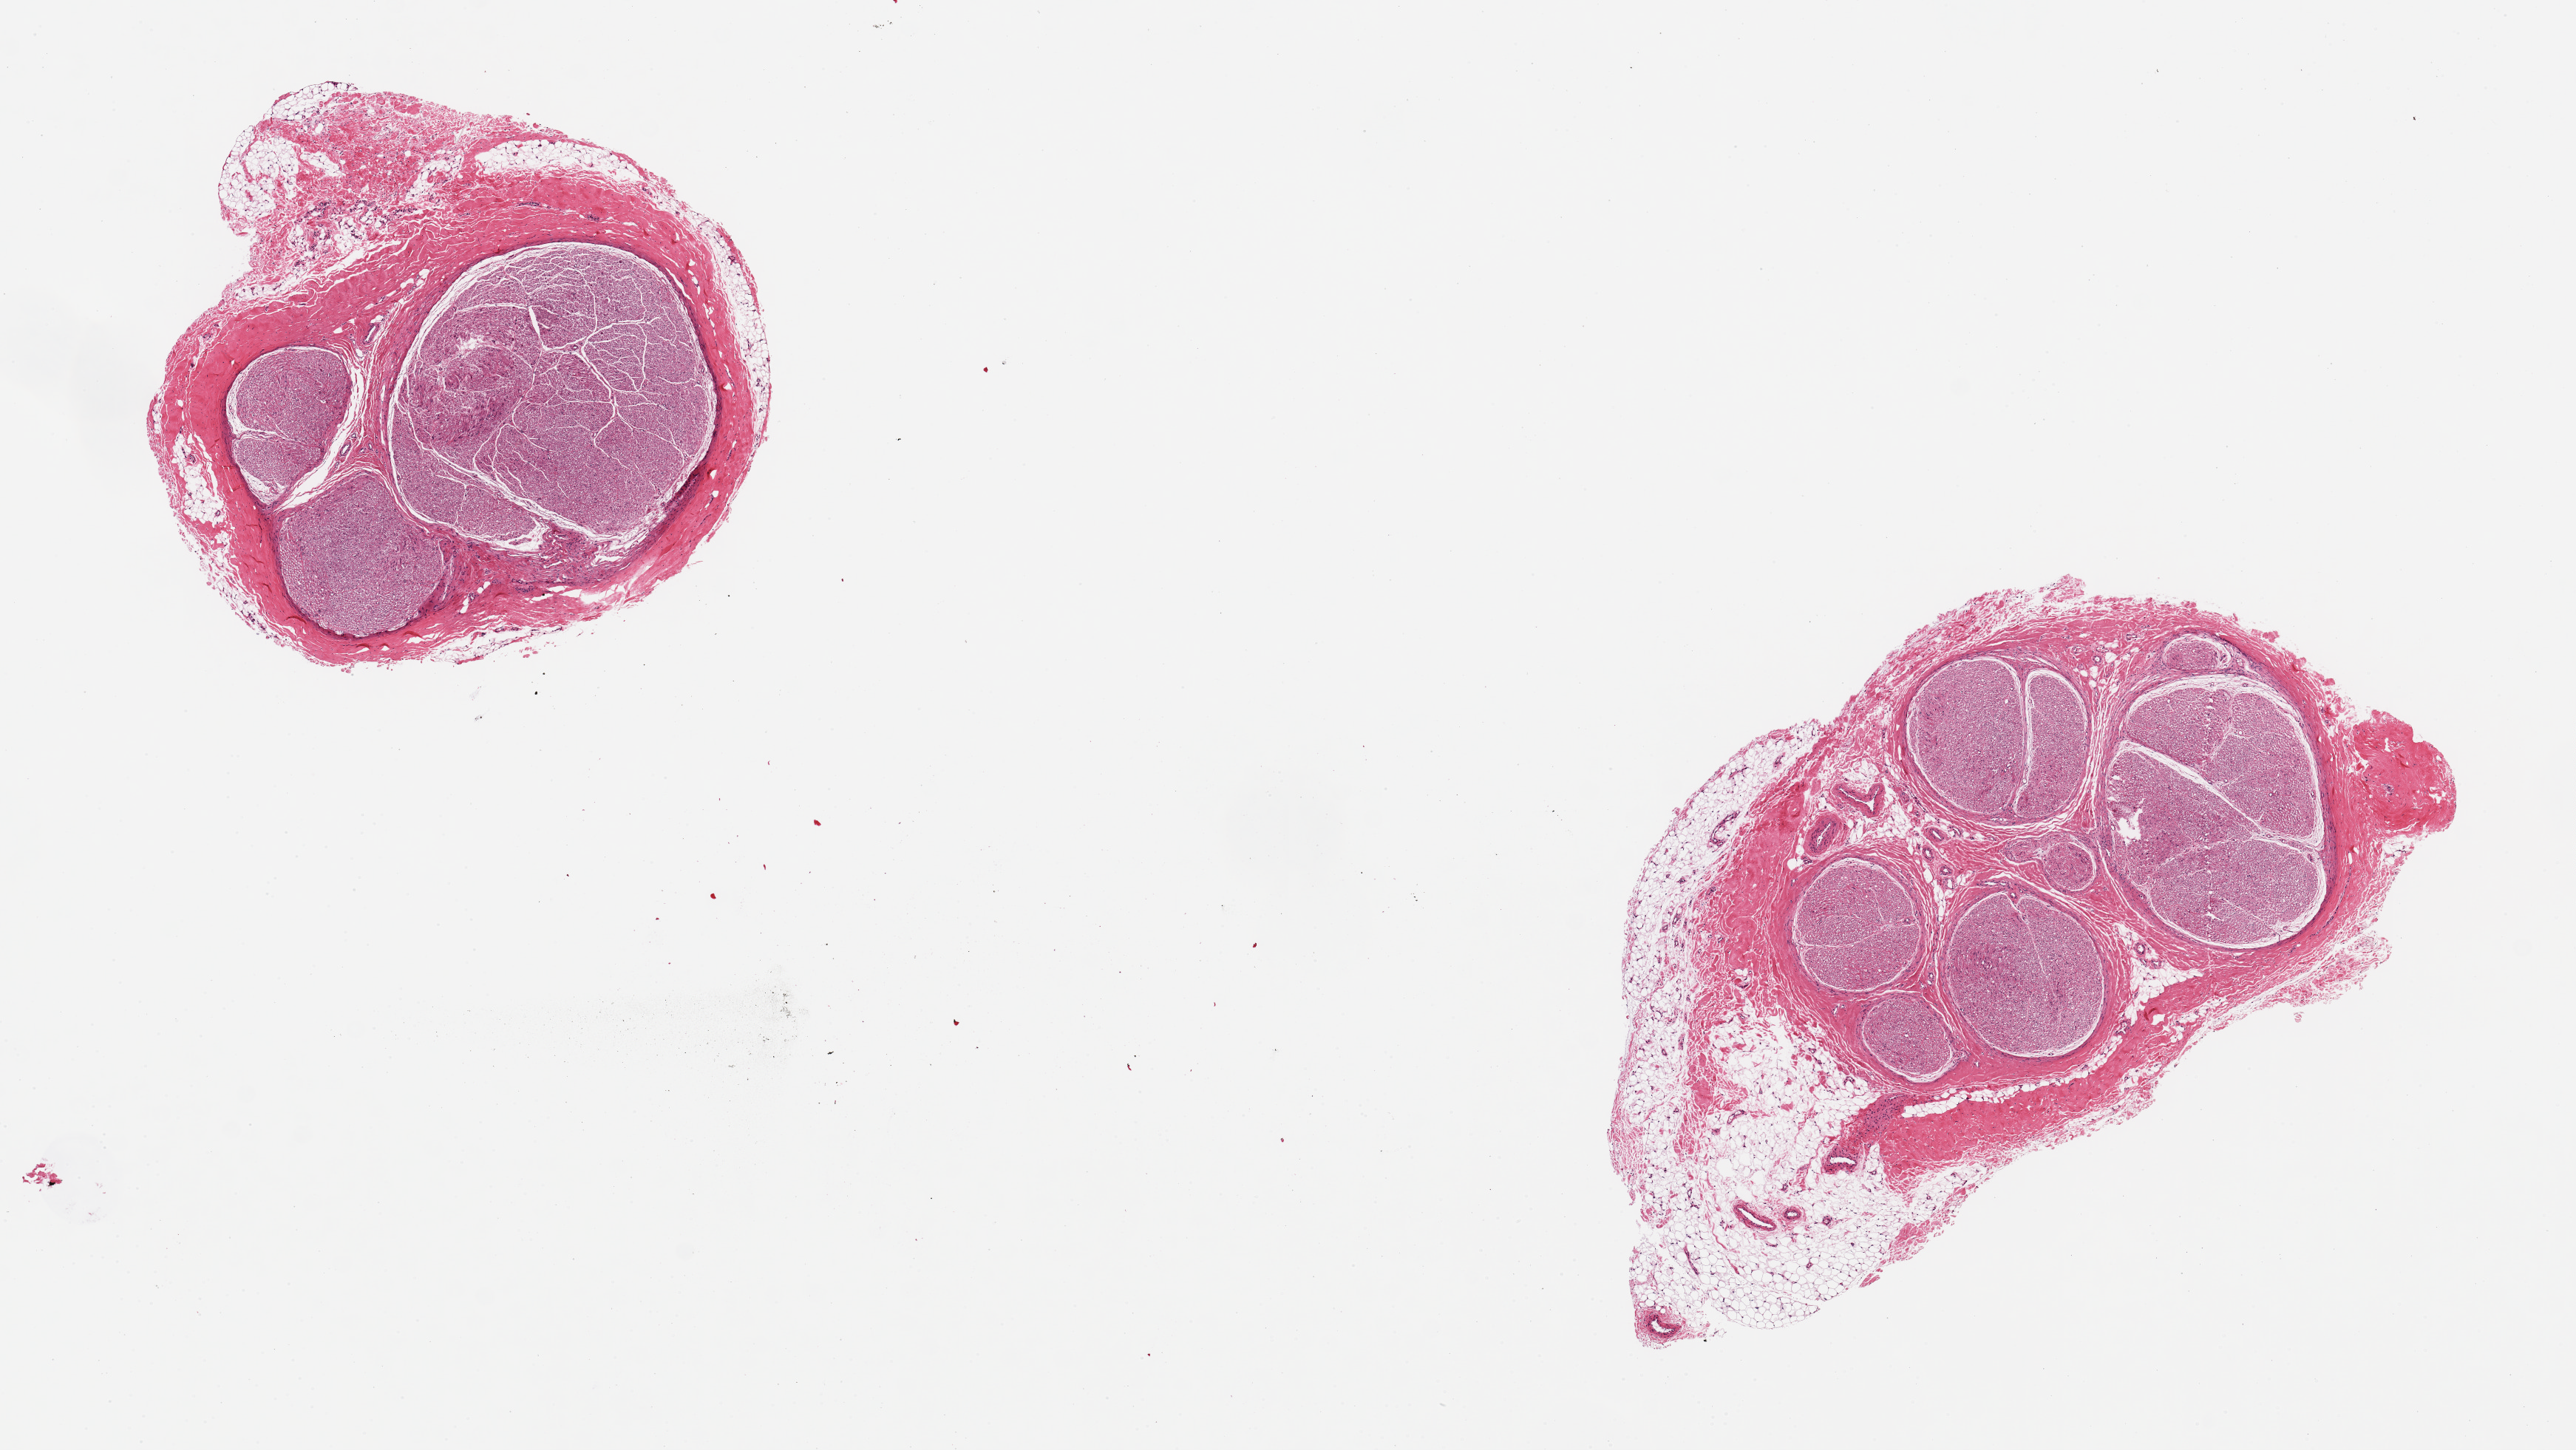
Whole-slide image, hematoxylin and eosin (H&E) stain, whole scanned area (about 13.8 x 7.8 mm) shown as a low-resolution overview. Donor: male.
- specimen: PAXgene-fixed, paraffin-embedded tissue; target tissue: tibial nerve; donor tissue sample